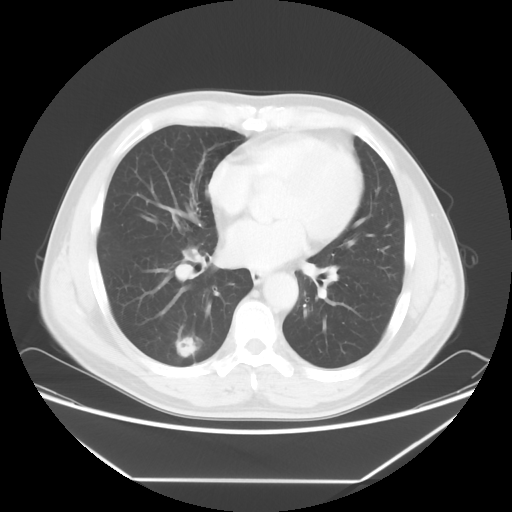
Chest CT, one axial slice. Slice 30 of 65 in the series (ordered by position). Lung window (W 1500 / L -600 HU). 5 mm slice thickness. 512 × 512 image matrix, field of view 418 × 418 mm. Male patient, age 50 years. Case-level facts recorded for this patient, not image findings: clinical TNM (as recorded): T1c N0 M0; histopathological grade: G3.
Annotated regions visible in this slice (bounding box drawn by a radiologist):
- lung tumour (recorded histology: adenocarcinoma): bounding box <169,332,208,361> (left, top, right, bottom; pixels)